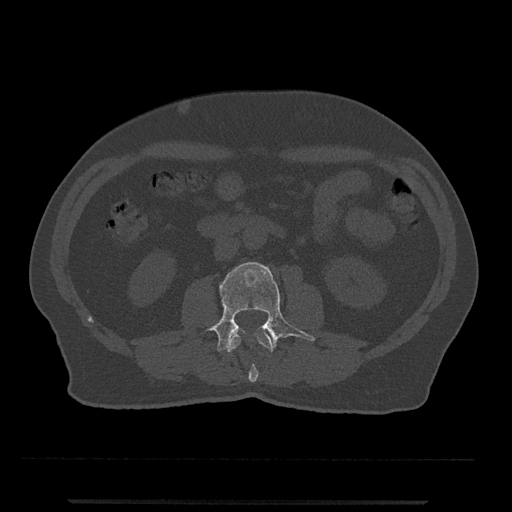
CT including the spine, one axial slice; position 217 of 797 along the scan axis; reconstruction kernel Br40s/3; bone window (W 1800 / L 400 HU); 0.5 mm slice thickness; 512 × 512 image matrix, field of view 419 × 419 mm. Male patient, age 63 years. From the clinical record (not read from this slice): primary cancer: prostate.
Outlined on this slice (semi-automatically segmented with operator editing):
- L2 vertebra: bounding box <227,332,273,382> (left, top, right, bottom; pixels)
- L3 vertebra: <209,262,315,352>